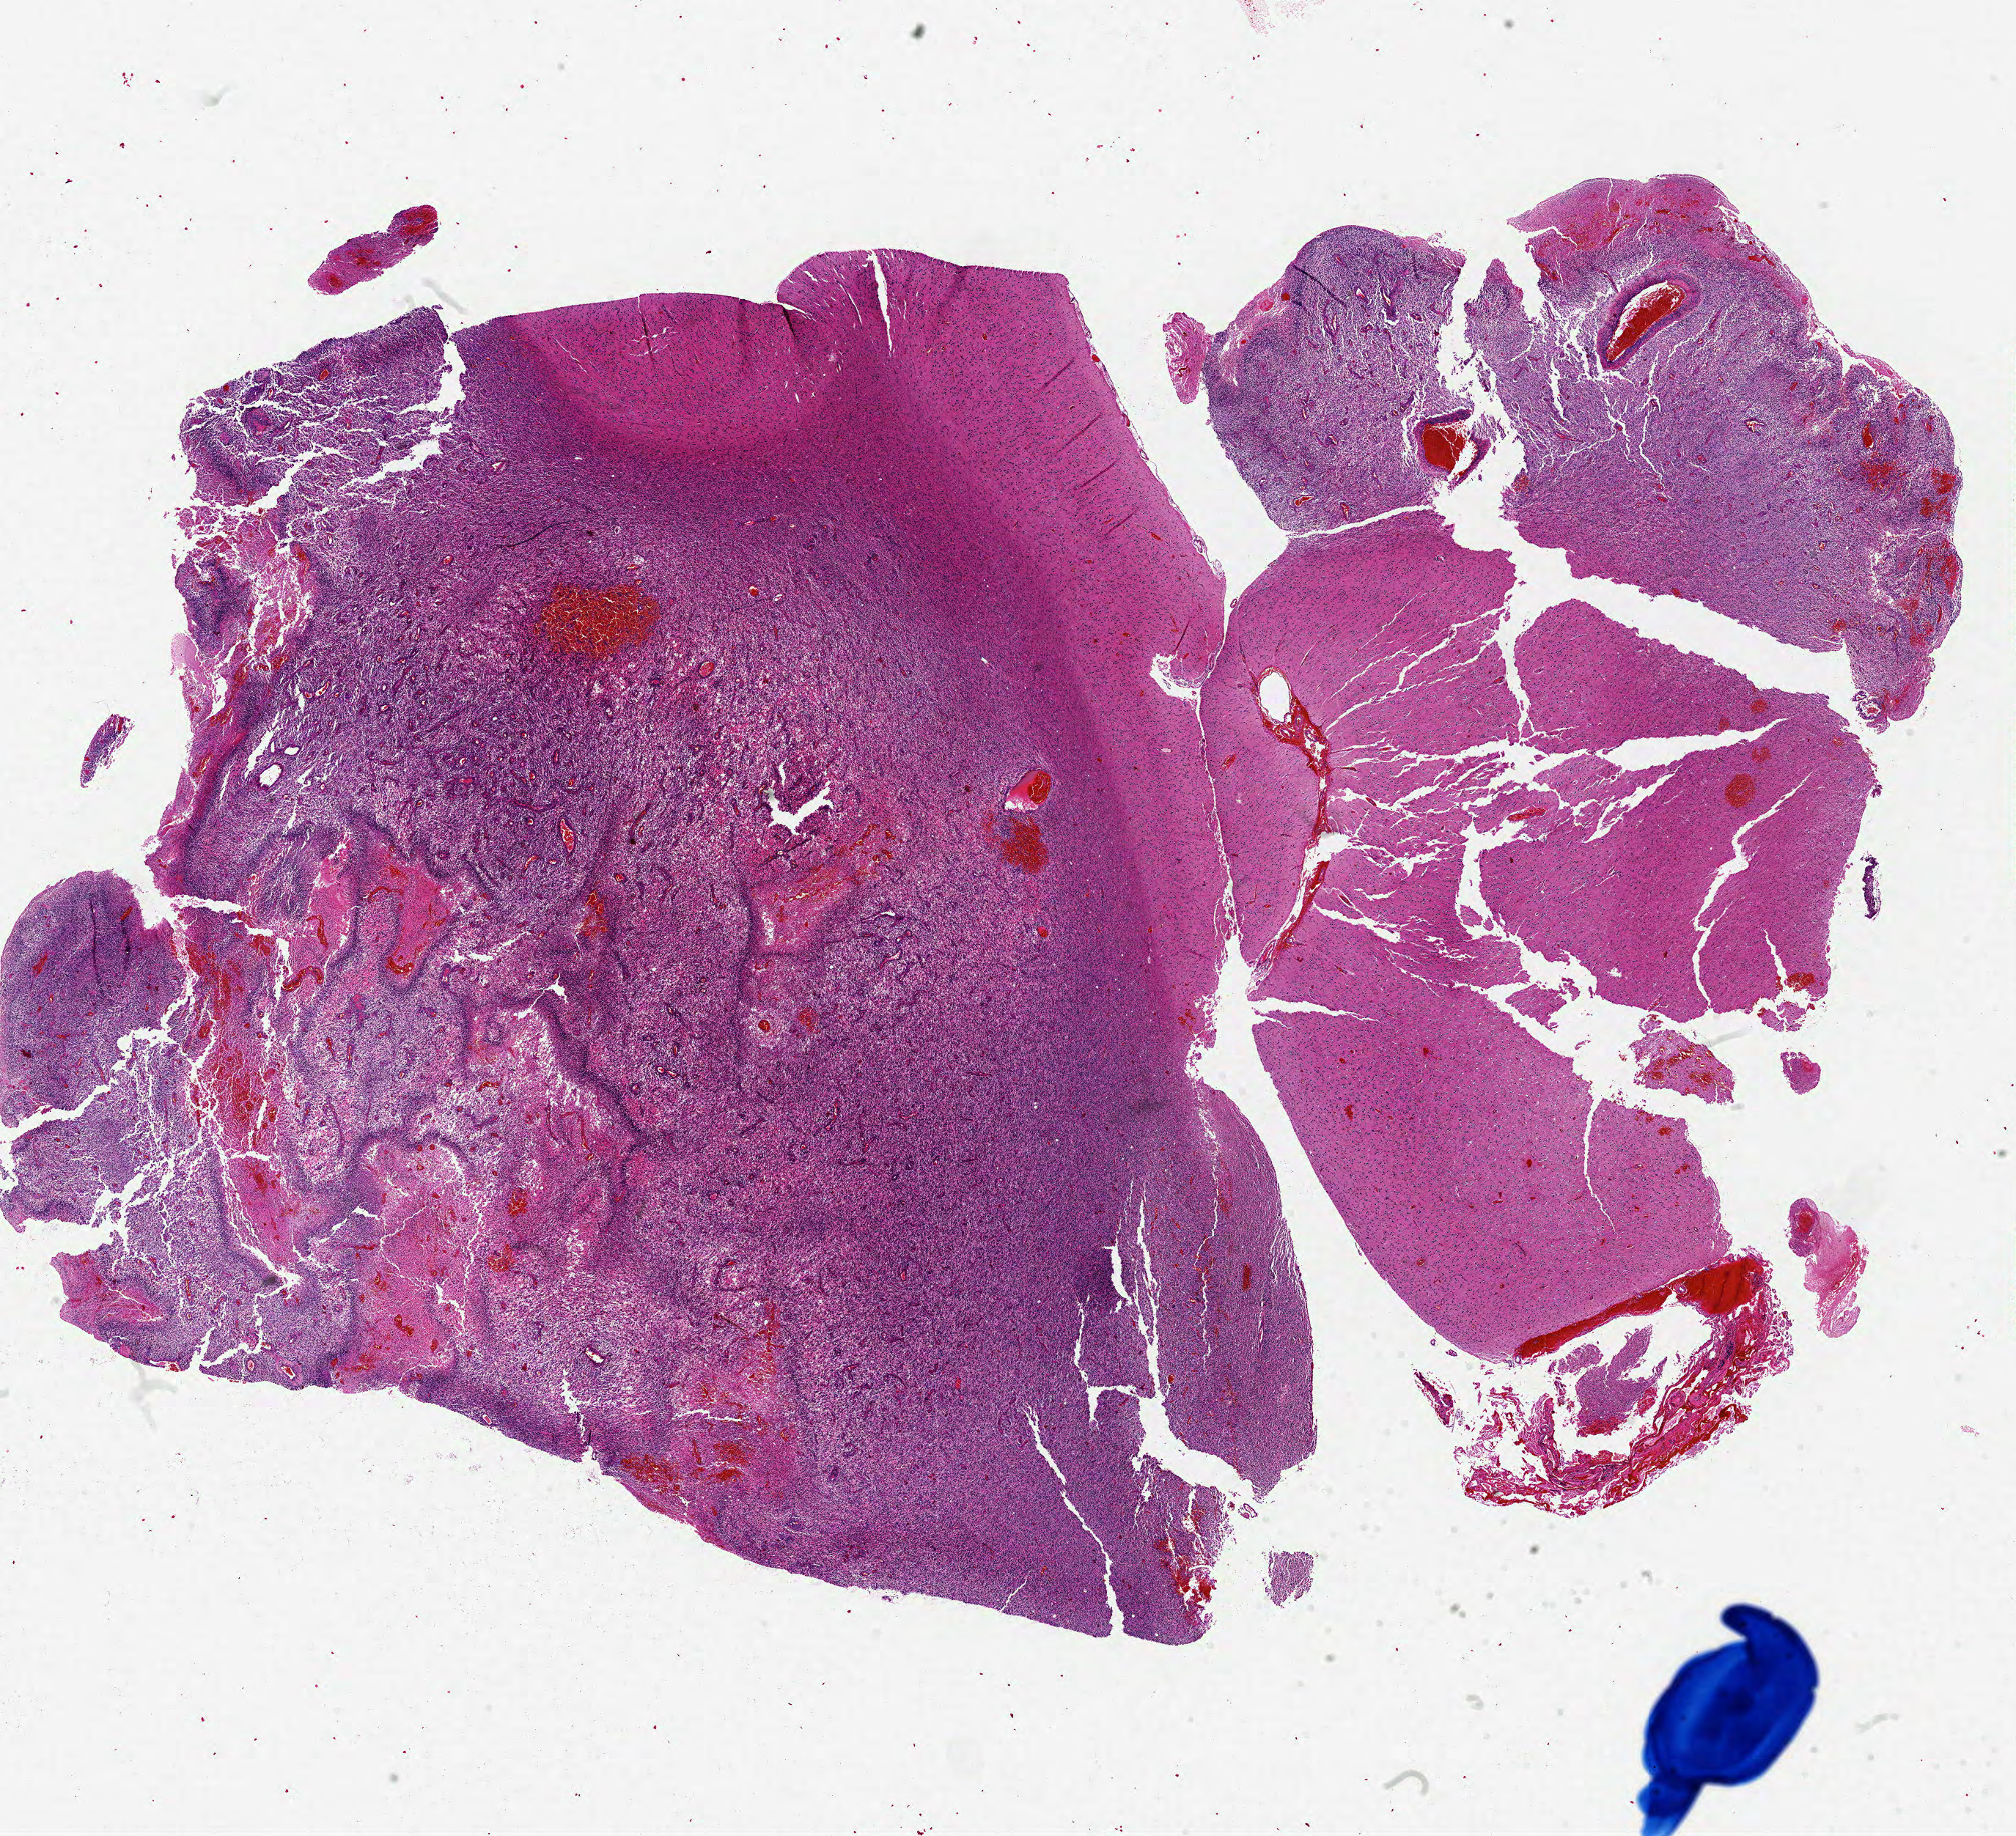
Digitized H&E tissue section (whole slide), a low-resolution overview of the entire scanned area, about 22.0 x 20.0 mm. Formalin-fixed paraffin-embedded (FFPE) diagnostic section. Sample: primary tumour, brain. Female, age 51 years at initial diagnosis.
* pathologic diagnosis: Glioblastoma